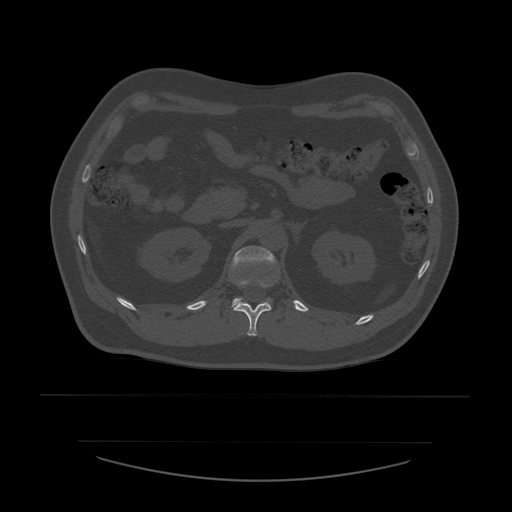
CT including the spine, one axial slice; slice 241 of 532 in the series (ordered by position); reconstruction kernel STANDARD; 120 kVp; bone window (W 1800 / L 400 HU); 1.25 mm slice thickness; 512 × 512 image matrix. Patient age 44 years. Case-level facts recorded for this patient, not image findings: primary cancer: soft tissue sarcoma.
Outlined on this slice (semi-automatically segmented with operator editing):
- L1 vertebra: bounding box [x1, y1, x2, y2] px = [232, 246, 276, 308]
- T12 vertebra: [234, 283, 272, 337]